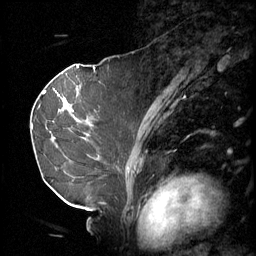
Breast MRI (dynamic contrast-enhanced), one sagittal slice. Slice 33 of 60 in the series (ordered by position). 3 images stored at this slice position (order not interpretable as contrast timing). 1.5 T. TE 4.2 ms, TR 11 ms. 256 × 256 image matrix, field of view 220 × 220 mm. Female patient, age 69 years.
Annotated regions visible in this slice (semi-automatic segmentation, software-assisted and operator-edited):
- analysis volume of interest (the breast-tissue region the enhancement analysis was run in; not a lesion): bounding box (x1, y1, x2, y2) in pixels: (36, 88, 102, 189)
- tumour enhancement mask (voxels above the 70 % enhancement threshold inside the analysis volume of interest): (63, 98, 89, 125)